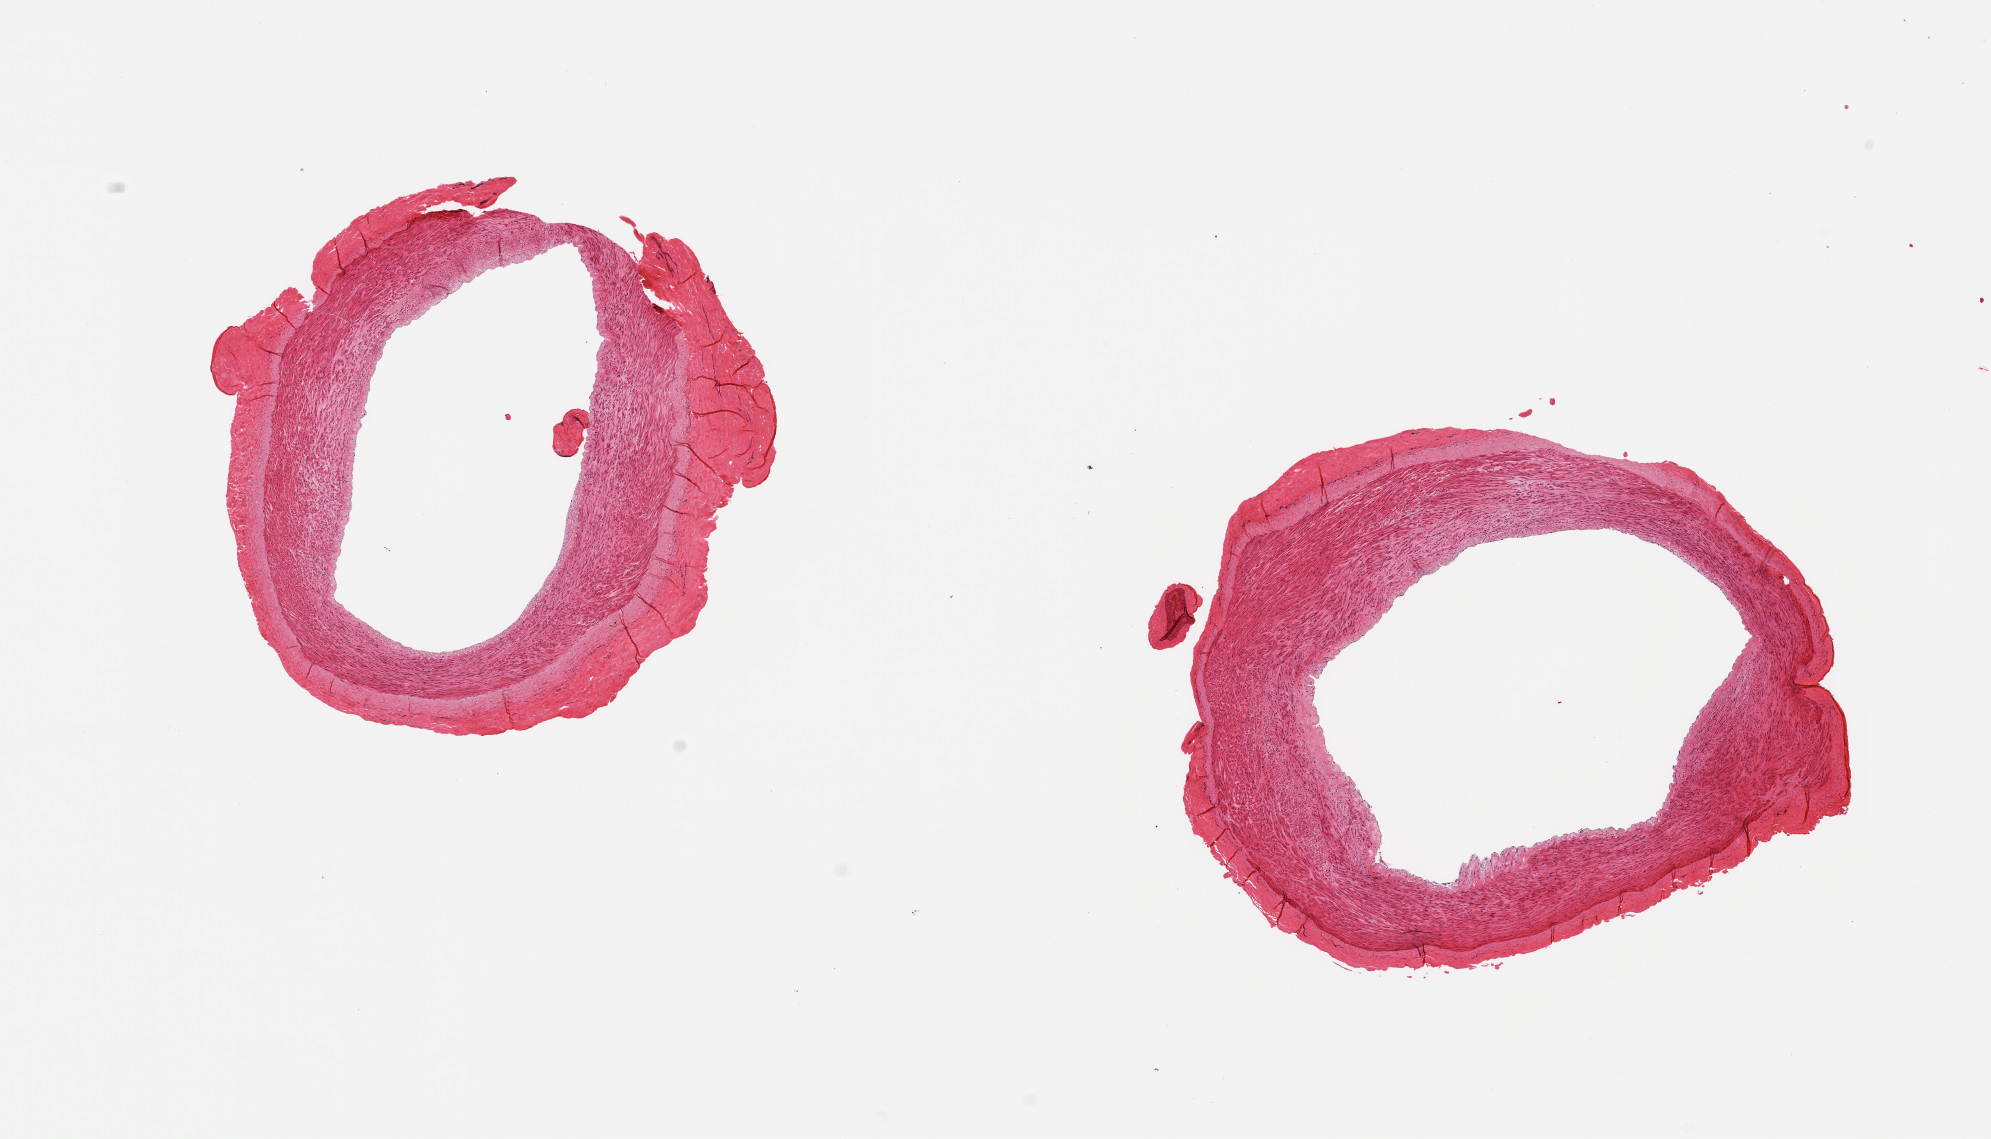
Whole-slide image, H&E stain — shown as a low-resolution overview of the whole scanned area (about 15.8 x 9.0 mm, slide scanned at 20x), PAXgene-fixed, paraffin-embedded tissue, sampled site (target tissue): tibial artery, donor tissue sample. Donor: male.
- pathologist's review note for this sample: 2 pieces